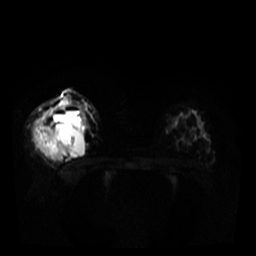
Breast MRI, one axial slice; diffusion-weighted series; image 2 of 4 stored at this slice position (different b-values; order by instance number); 3 T; 5 mm slice thickness; 256 × 256 image matrix, field of view 320 × 320 mm. Female patient.
Structures marked on this image (manually delineated by an expert):
- tumour on diffusion-weighted imaging: box from (x=41, y=141) to (x=72, y=160) px